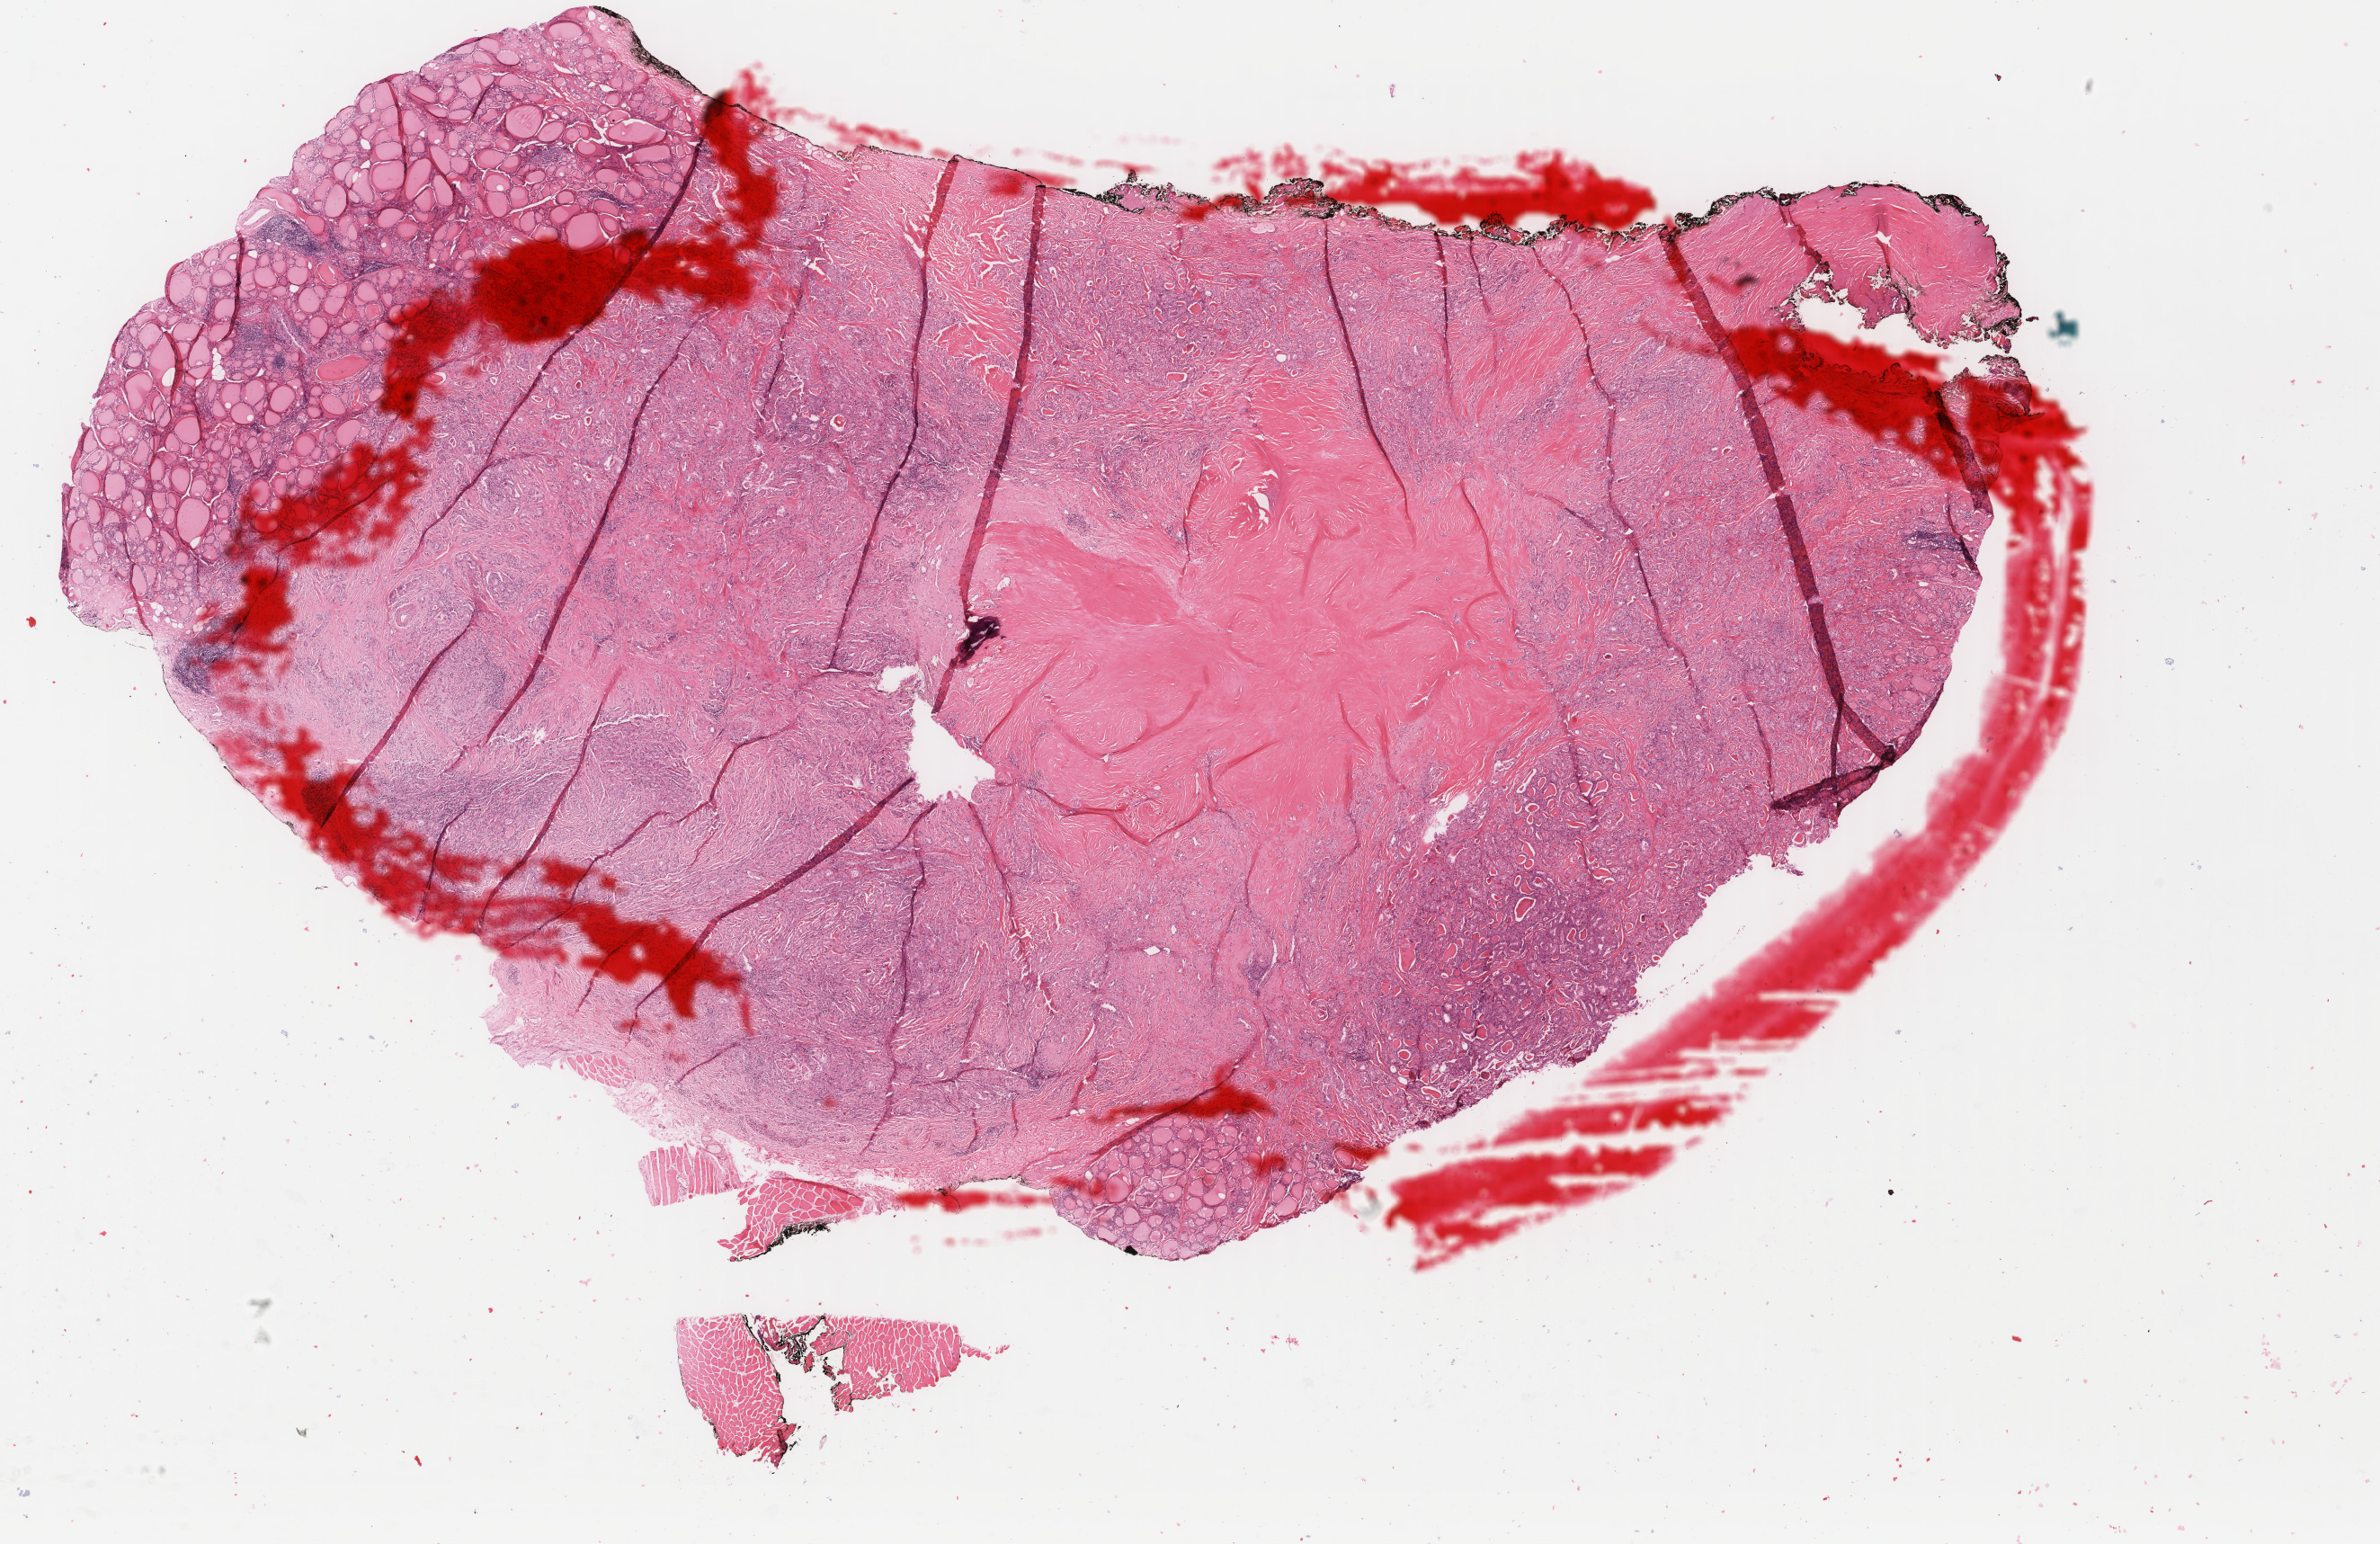
Digitized H&E-stained tissue section (whole slide), a low-resolution overview of the entire scanned area, about 21.0 x 13.6 mm (acquisition: 40x scan), formalin-fixed paraffin-embedded (FFPE) diagnostic section, sample: primary tumour, thyroid. Patient: female, age at initial diagnosis 56 years.
Diagnosis: Papillary adenocarcinoma, NOS (thyroid gland). AJCC pathologic stage: III (7th edition). Laterality: left. Lymph nodes positive (case pathology): 0 of 1 examined.